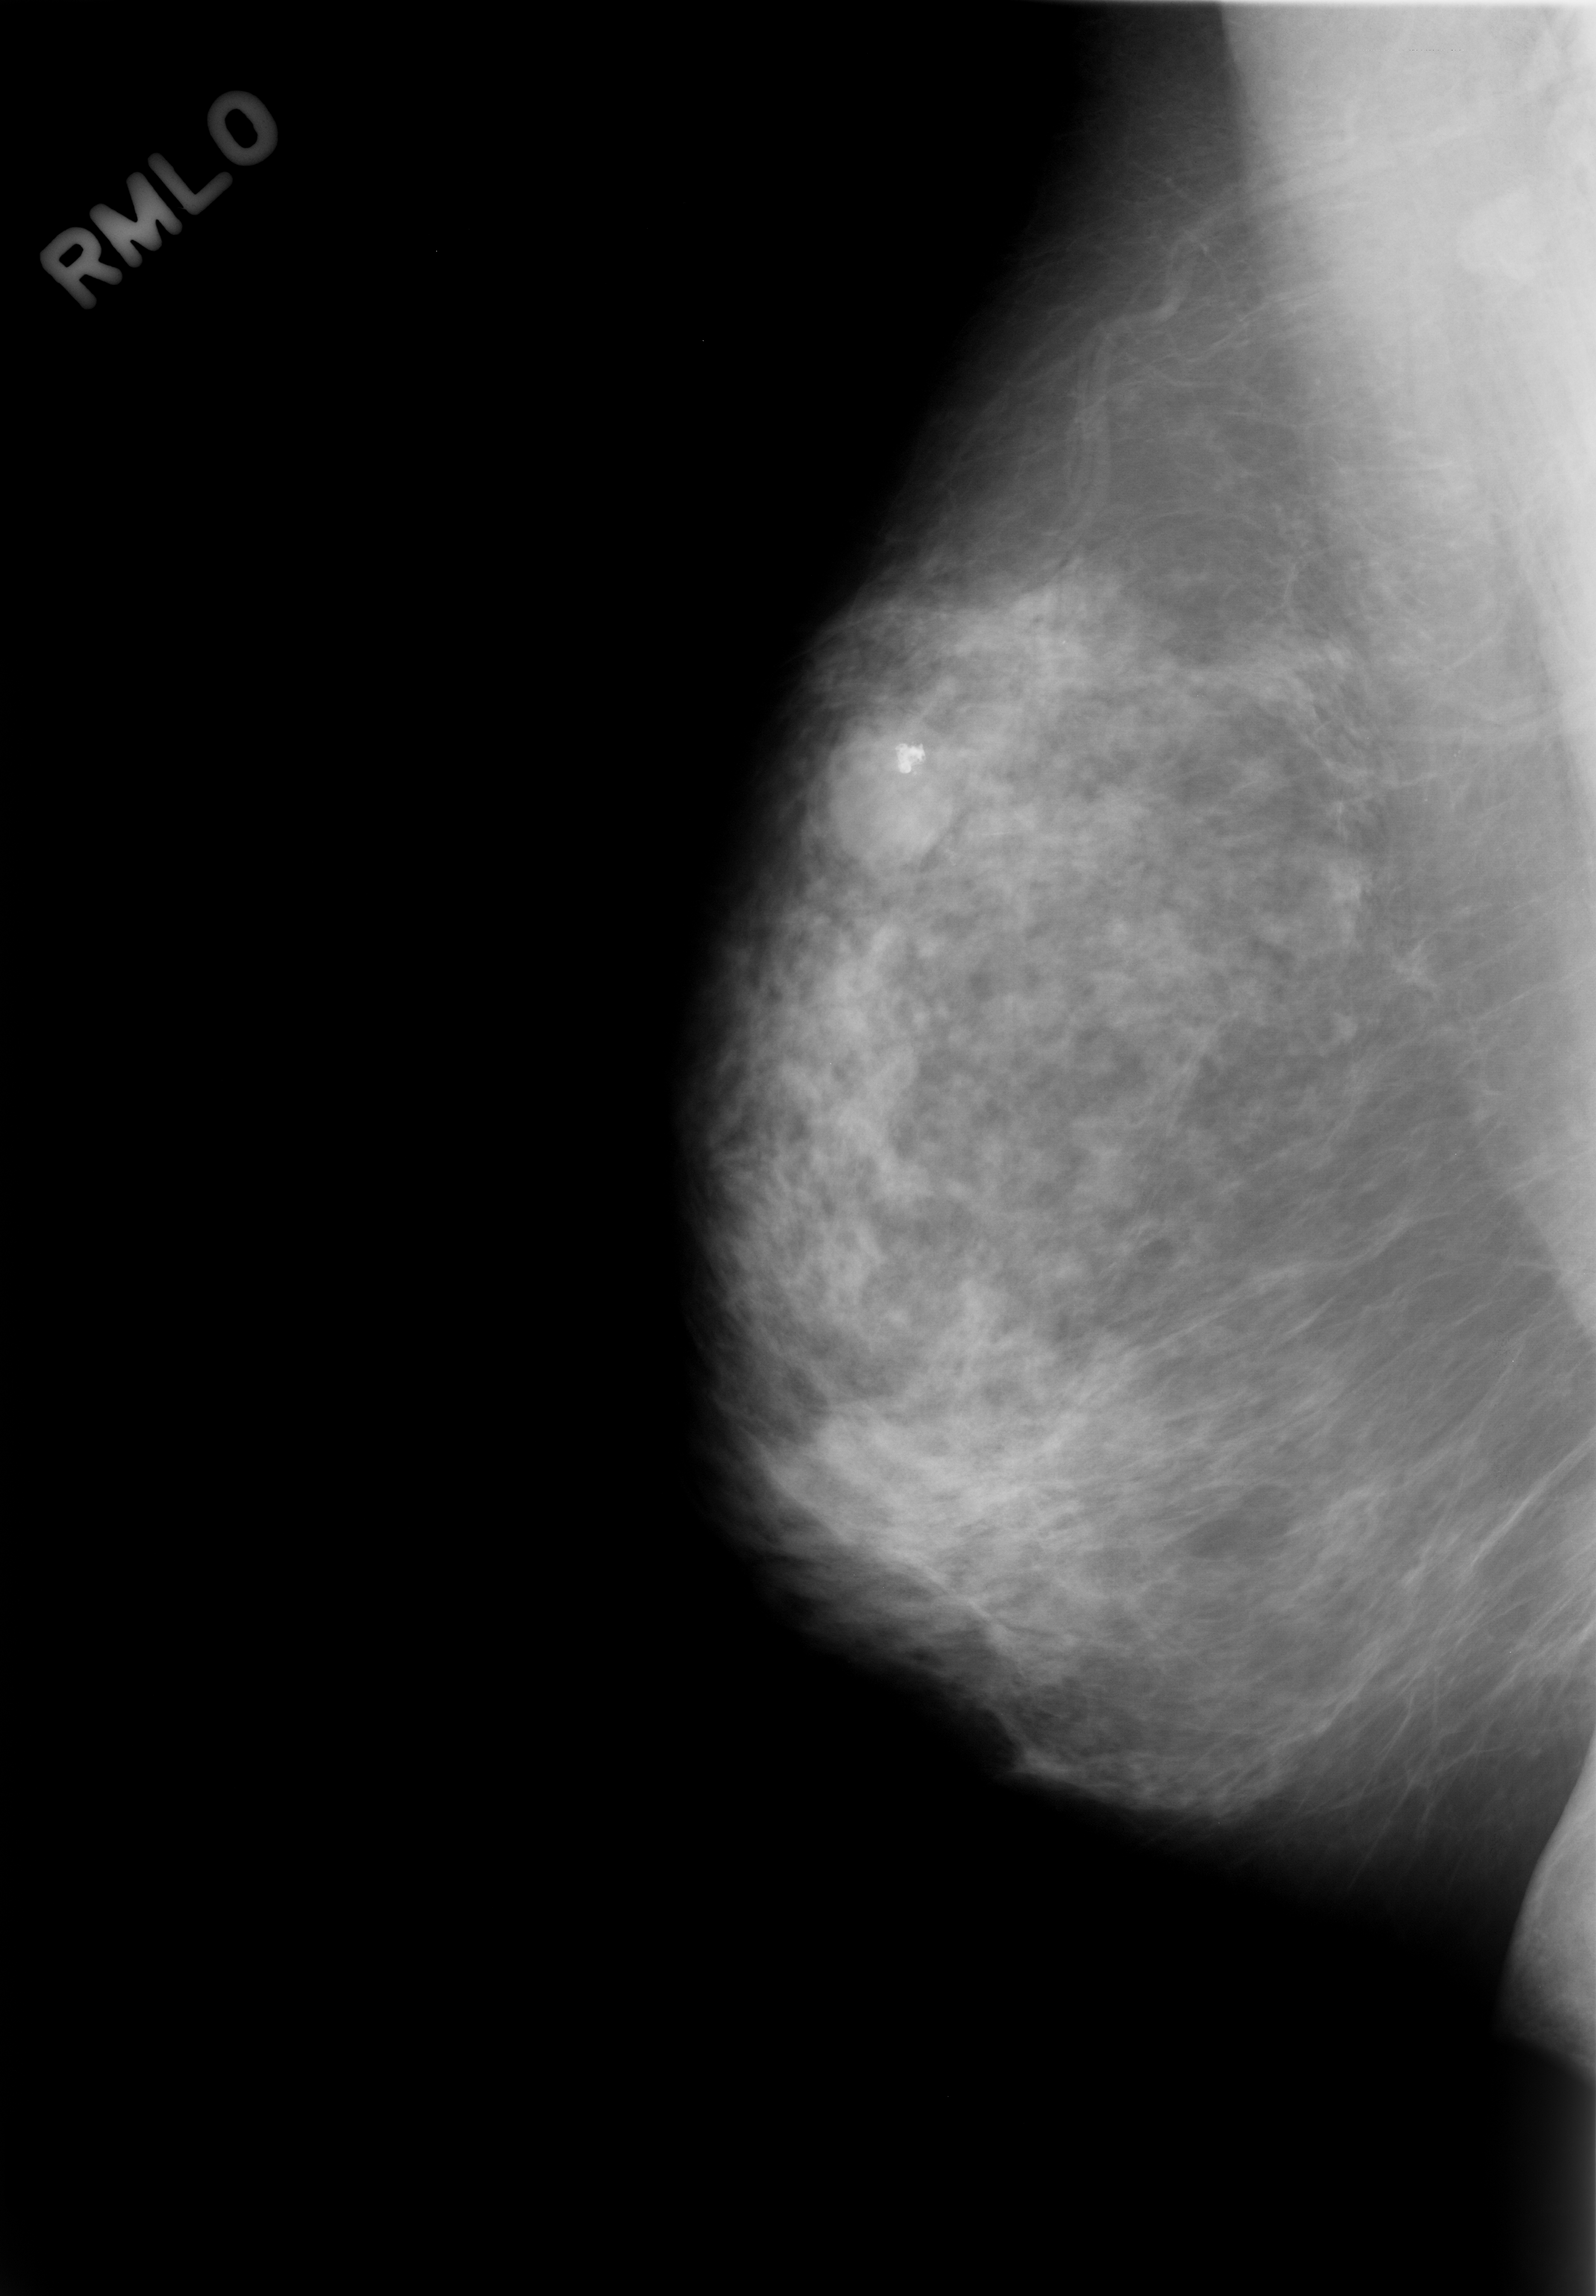
Digitized screen-film mammogram; right breast; MLO view.
Radiologist-marked abnormalities on this image: mass, shape oval, margins microlobulated; BI-RADS assessment category 4; pathology result (as recorded, not read from the image): benign.